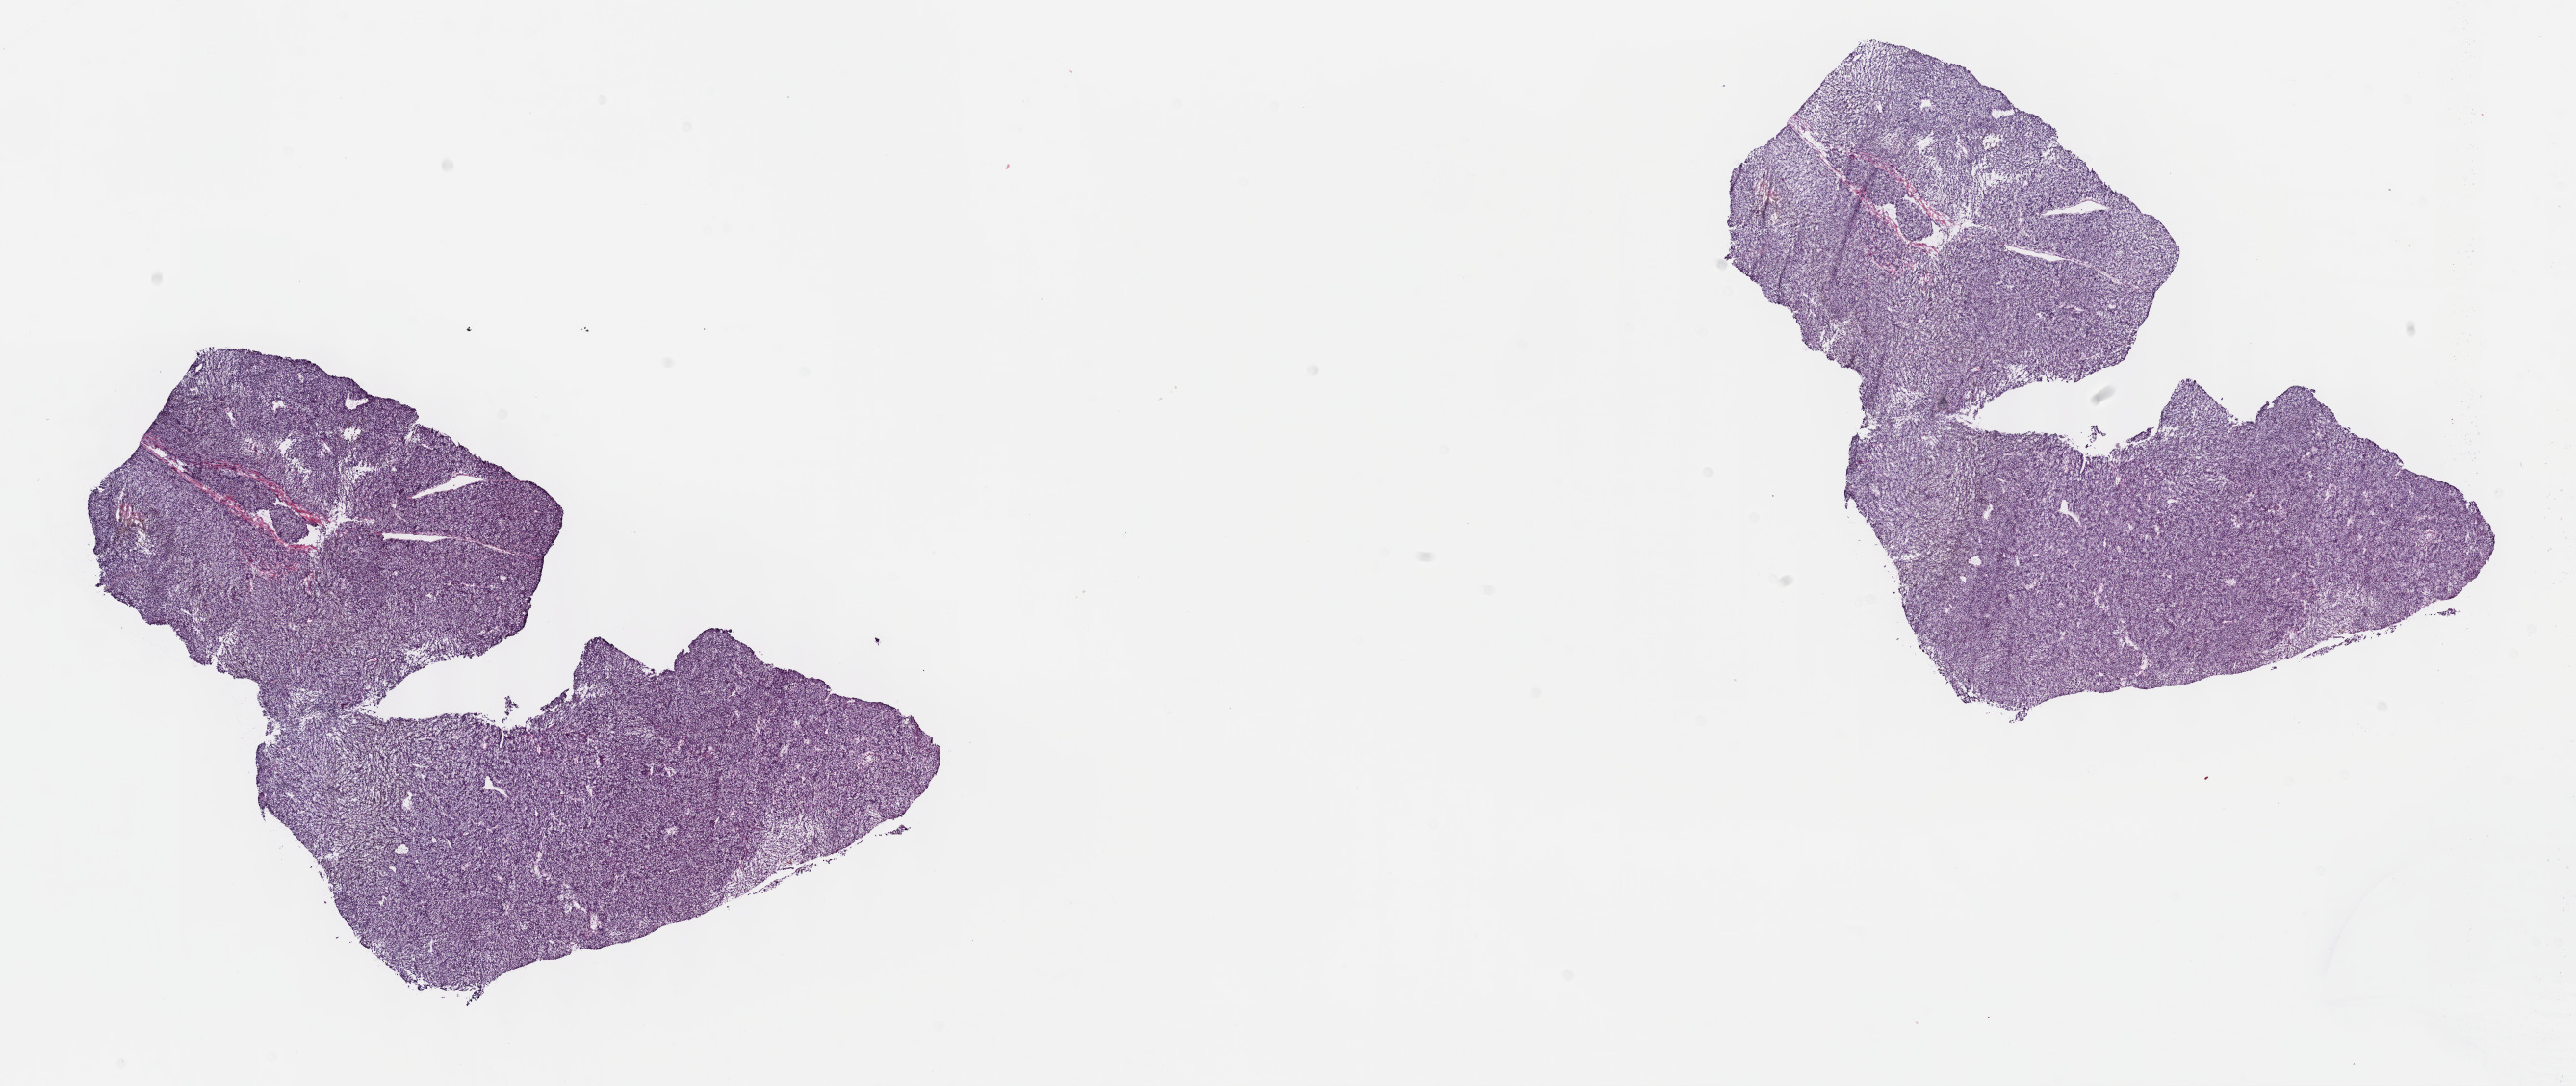
Digitized Hematoxylin and eosin (H&E) stained tissue section (whole slide), shown as a low-resolution overview of the whole scanned area (about 21.6 x 9.1 mm, slide scanned at 40x); frozen section from the top of the tissue portion; sample: primary tumour, uvea. Patient: female, age at initial diagnosis 41 years. Slide review estimates, as recorded: tumour cells 100%, tumour nuclei 80%, normal cells 0%, stromal cells 0%, necrosis 0%. Infiltration values recorded for this section: lymphocyte infiltration 2%, monocyte infiltration 0%, neutrophil infiltration 0%.
• laterality: right
• histologic diagnosis: Spindle cell melanoma, NOS (choroid)
• AJCC pathologic stage: IIIA